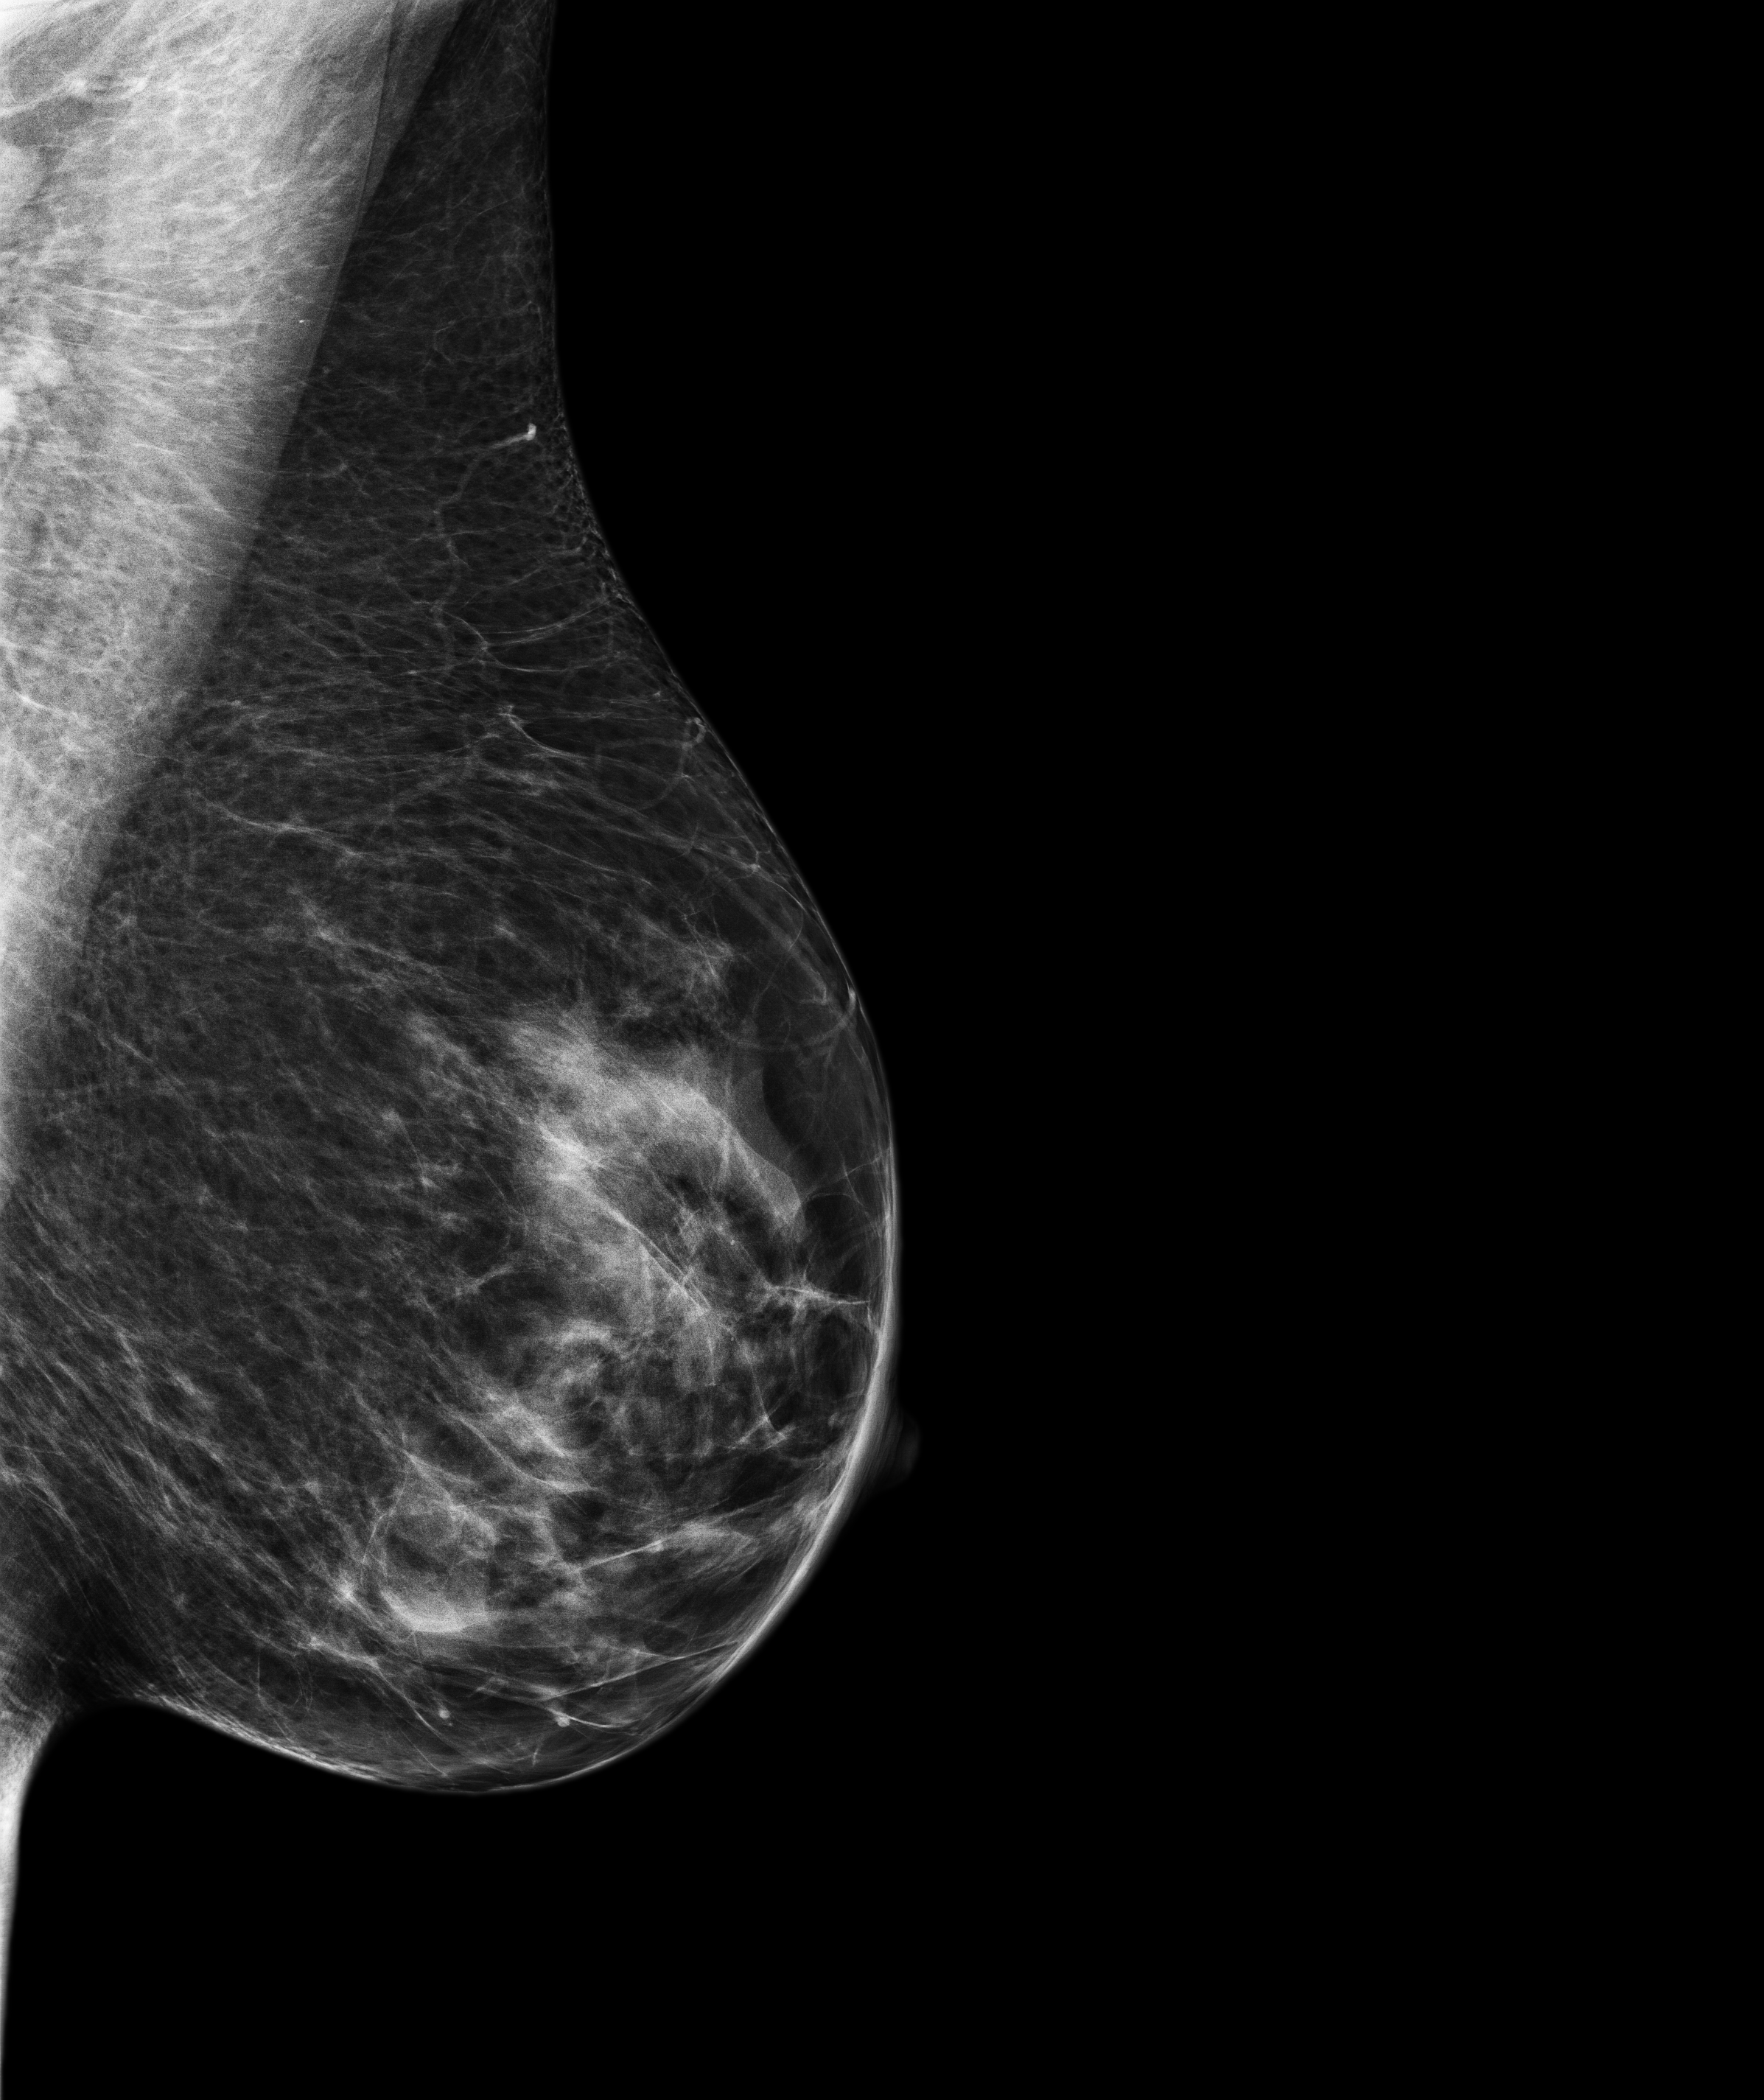
Screening examination, compressed breast thickness 72.6 mm, system: Senographe Pristina. Patient aged 49 years (female).
Image type: full-field digital mammogram. Breast: left. Projection: medio-lateral oblique projection.